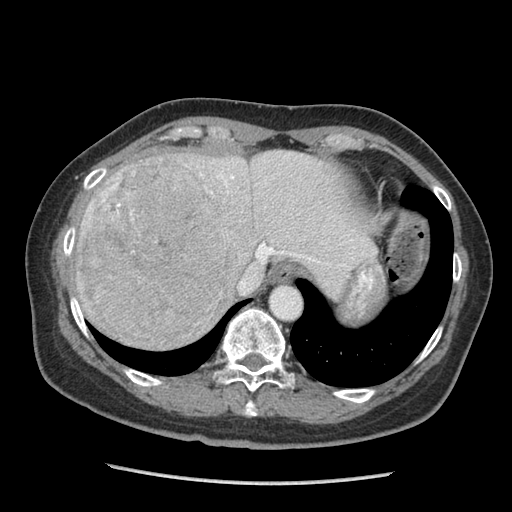
Contrast-enhanced abdominal CT (liver protocol), one axial slice; slice 74 of 105 in the series (ordered by position); reconstruction kernel STANDARD; soft-tissue window (W 400 / L 40 HU); 512 × 512 image matrix. From the clinical record (not read from this slice): diagnosis: hepatocellular carcinoma (patient treated with transarterial chemoembolisation; whether this scan precedes or follows treatment is not stated here); TNM stage (as recorded): Stage-I; Child-Pugh class: A; tumour differentiation: moderately differentiated; tumour nodularity: uninodular.
Outlined on this slice (semi-automatically segmented with operator editing):
- abdominal aorta: box from (x=272, y=287) to (x=300, y=318) px
- liver parenchyma outside the tumour (the mass and vessels are separate outlines, so this box may not span the whole liver): (x=72, y=150)–(x=360, y=324)
- mass: (x=75, y=156)–(x=230, y=349)
- liver vessels: (x=217, y=174)–(x=315, y=262)